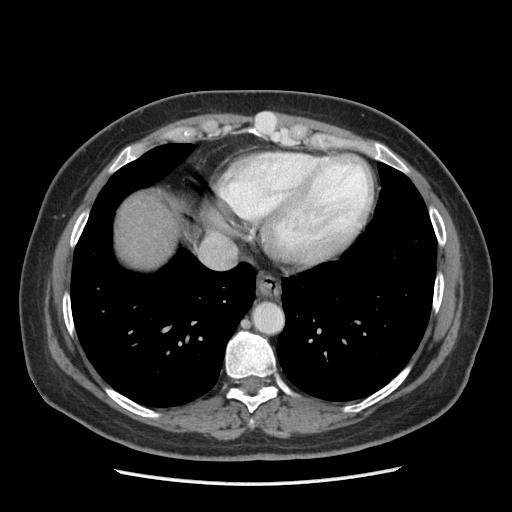
Contrast-enhanced abdominal CT (liver protocol), one axial slice; position 175 of 185 along the scan axis; reconstruction kernel STANDARD; soft-tissue window (W 400 / L 40 HU); 2.5 mm slice thickness; 512 × 512 image matrix, field of view 360 × 360 mm. From the clinical record (not read from this slice): diagnosis: hepatocellular carcinoma (patient treated with transarterial chemoembolisation; whether this scan precedes or follows treatment is not stated here); TNM stage (as recorded): Stage-I; Child-Pugh class: A; tumour nodularity: uninodular.
Annotated regions visible in this slice (semi-automatic segmentation, software-assisted and operator-edited):
- liver parenchyma outside the tumour (the mass and vessels are separate outlines, so this box may not span the whole liver): box from (x=116, y=194) to (x=178, y=268) px